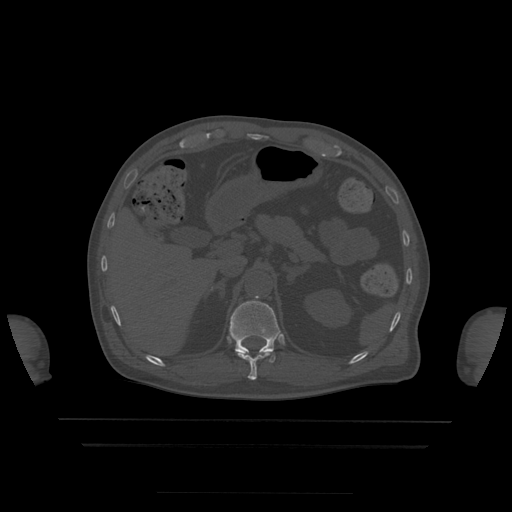
CT including the spine, one axial slice; slice 206 of 522 in the series (ordered by position); bone window (W 1800 / L 400 HU); 1.25 mm slice thickness; 512 × 512 image matrix, field of view 436 × 436 mm. Patient age 68 years. From the clinical record (not read from this slice): primary cancer: urothelial.
Structures marked on this image (semi-automatic segmentation, software-assisted and operator-edited):
- T11 vertebra: box from (x=236, y=352) to (x=275, y=380) px
- T12 vertebra: (x=230, y=296)–(x=281, y=361)